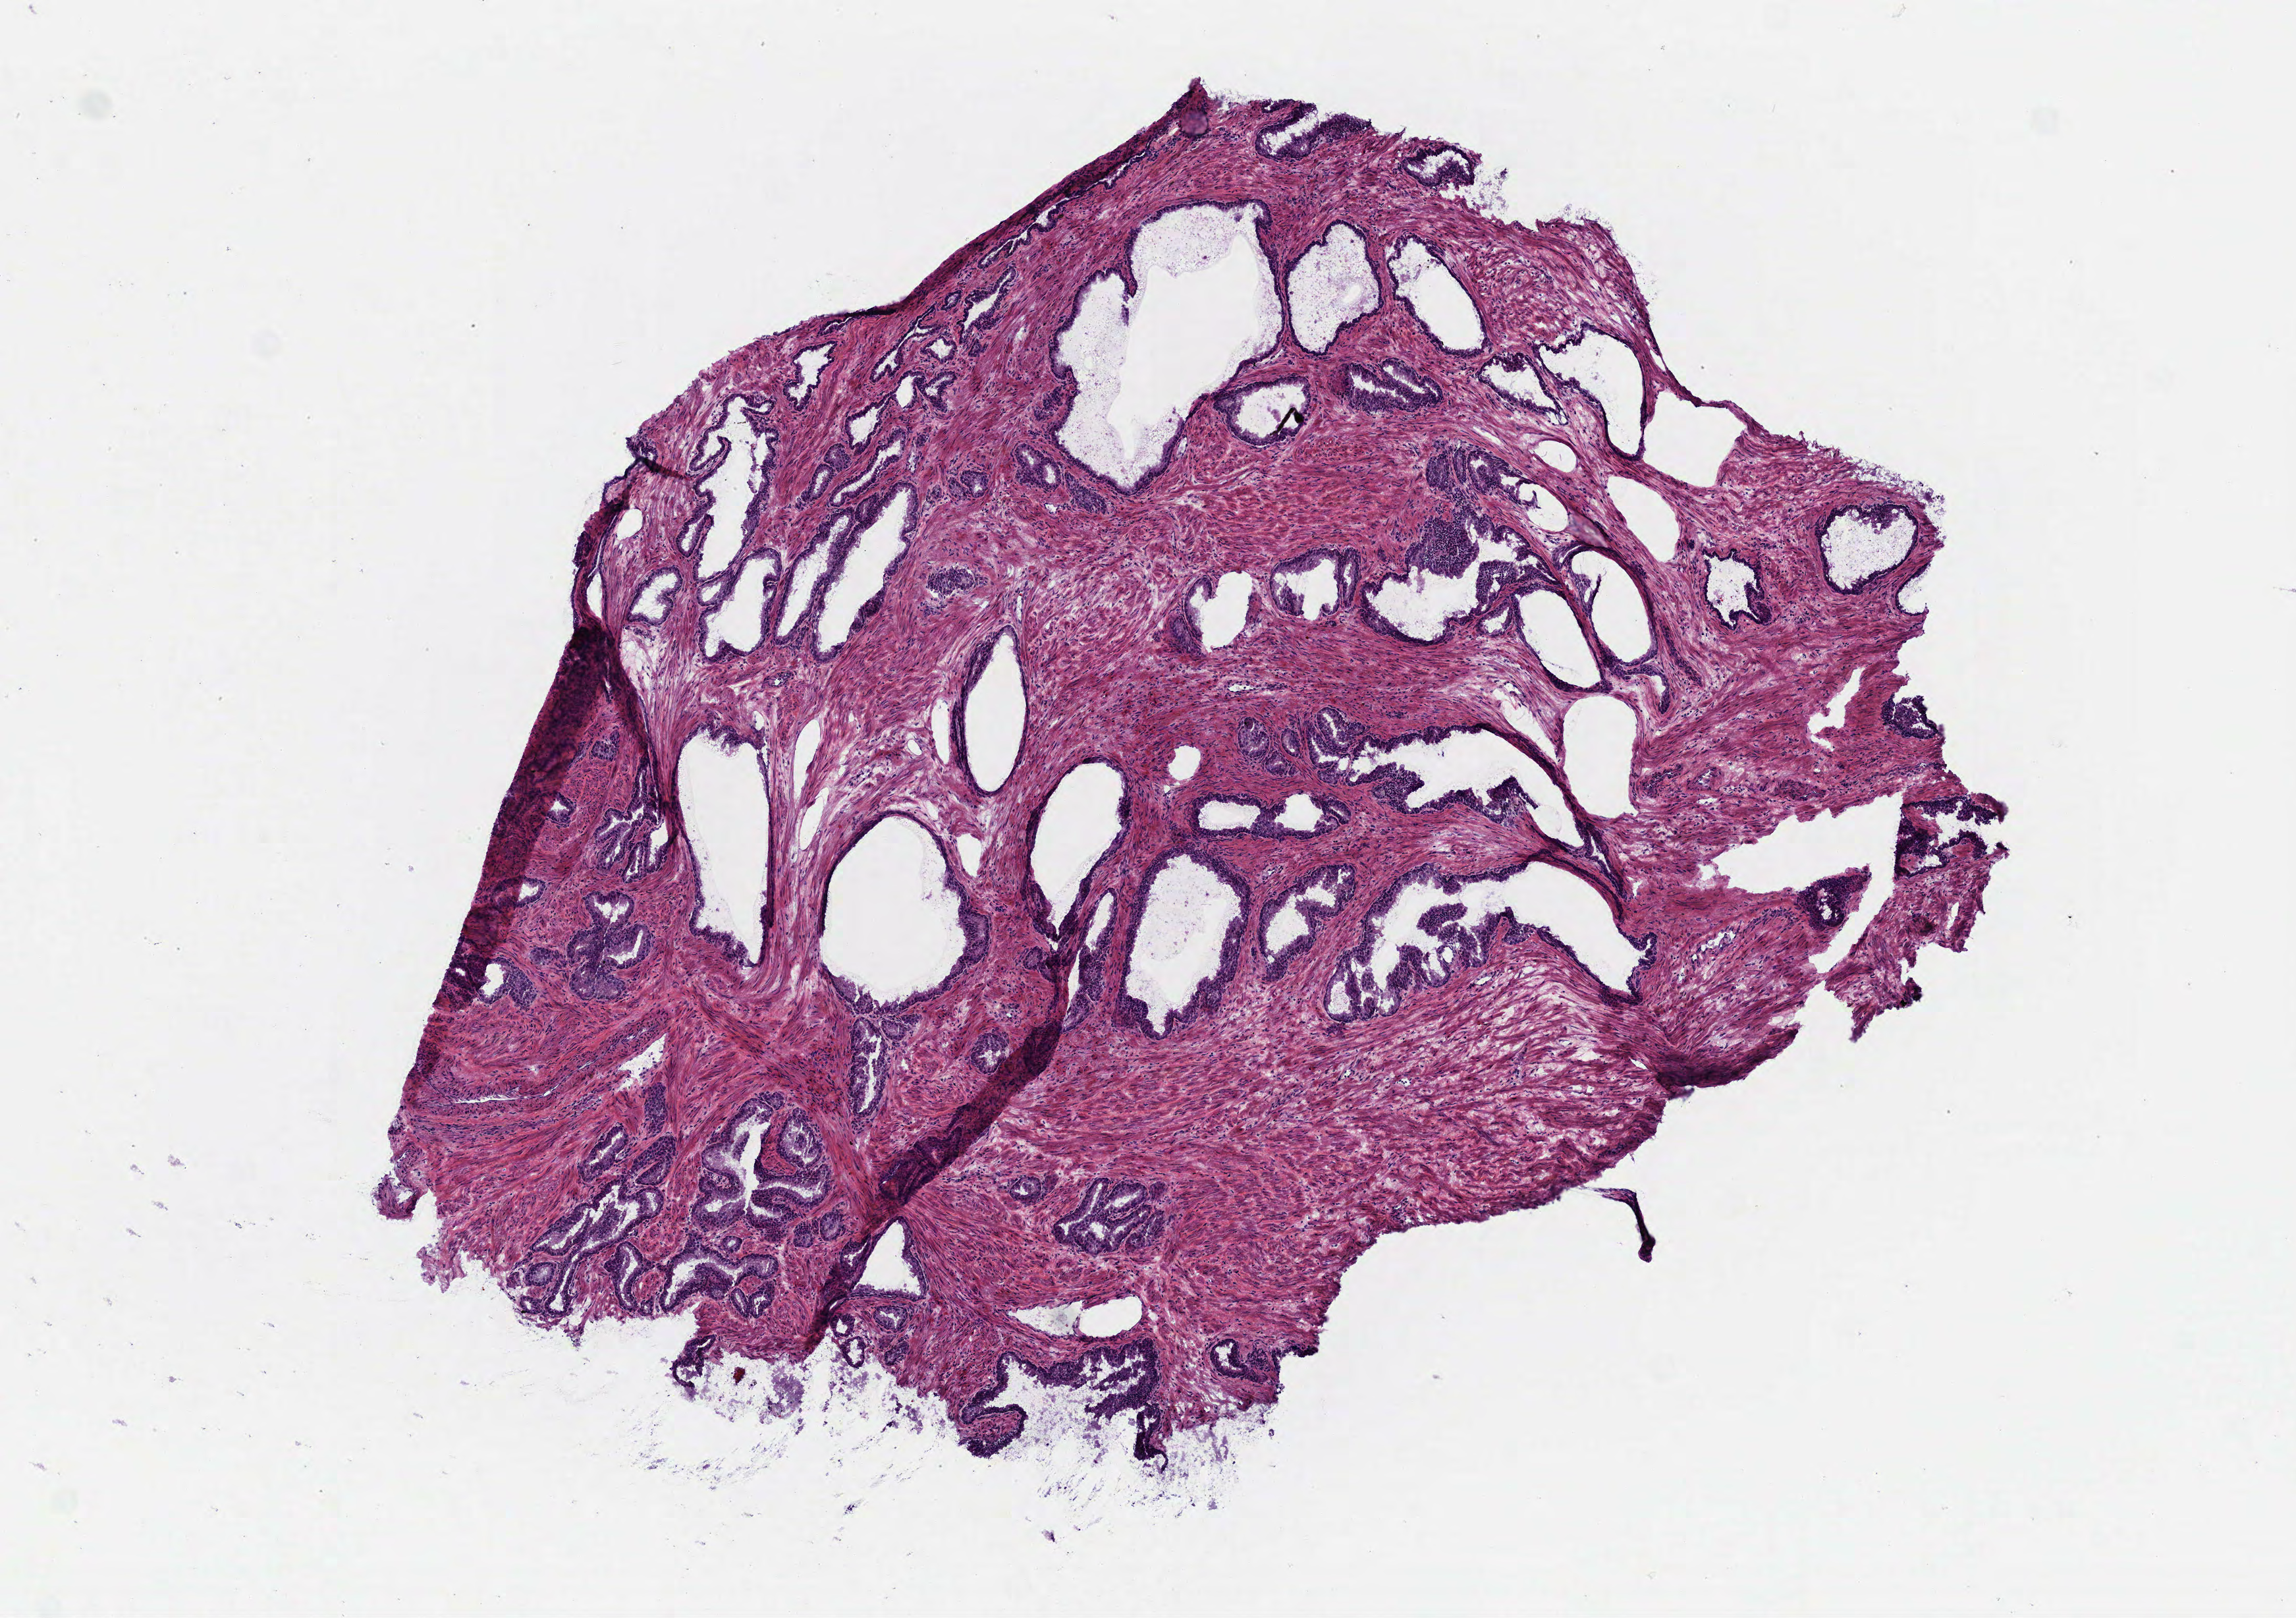
Whole-slide histology image, Hematoxylin and eosin (H&E) stained — whole scanned area (about 7.0 x 5.0 mm, acquisition: 40x scan) shown as a low-resolution overview, frozen section from the top of the tissue portion, solid tissue normal (non-tumour tissue) sample from the prostate. Patient: male, age at initial diagnosis 43 years.
This section: solid tissue normal sample (biorepository sample class). Patient diagnosis: Acinar cell carcinoma (prostate gland).